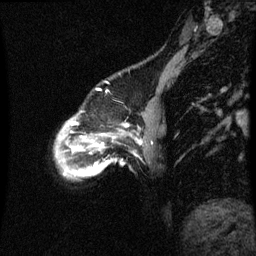
Breast MRI (dynamic contrast-enhanced), one sagittal slice. Position 11 of 60 along the scan axis. Dynamic contrast-enhanced series, image 2 of 3 at this slice position (ordered by acquisition). 1.5 T. TE 4.2 ms, TR 8.9 ms. 2 mm slice thickness. 256 × 256 image matrix, field of view 200 × 200 mm. Female patient, age 49 years. From the clinical record (not read from this slice): setting: breast cancer imaged before/during neoadjuvant chemotherapy; receptor status: HR-positive, HER2-negative.
Structures marked on this image (semi-automatic segmentation, software-assisted and operator-edited):
- analysis volume of interest (the breast-tissue region the enhancement analysis was run in; not a lesion): bounding box <56,112,127,179> (left, top, right, bottom; pixels)
- tumour enhancement mask (voxels above the 70 % enhancement threshold inside the analysis volume of interest): <78,148,81,151>